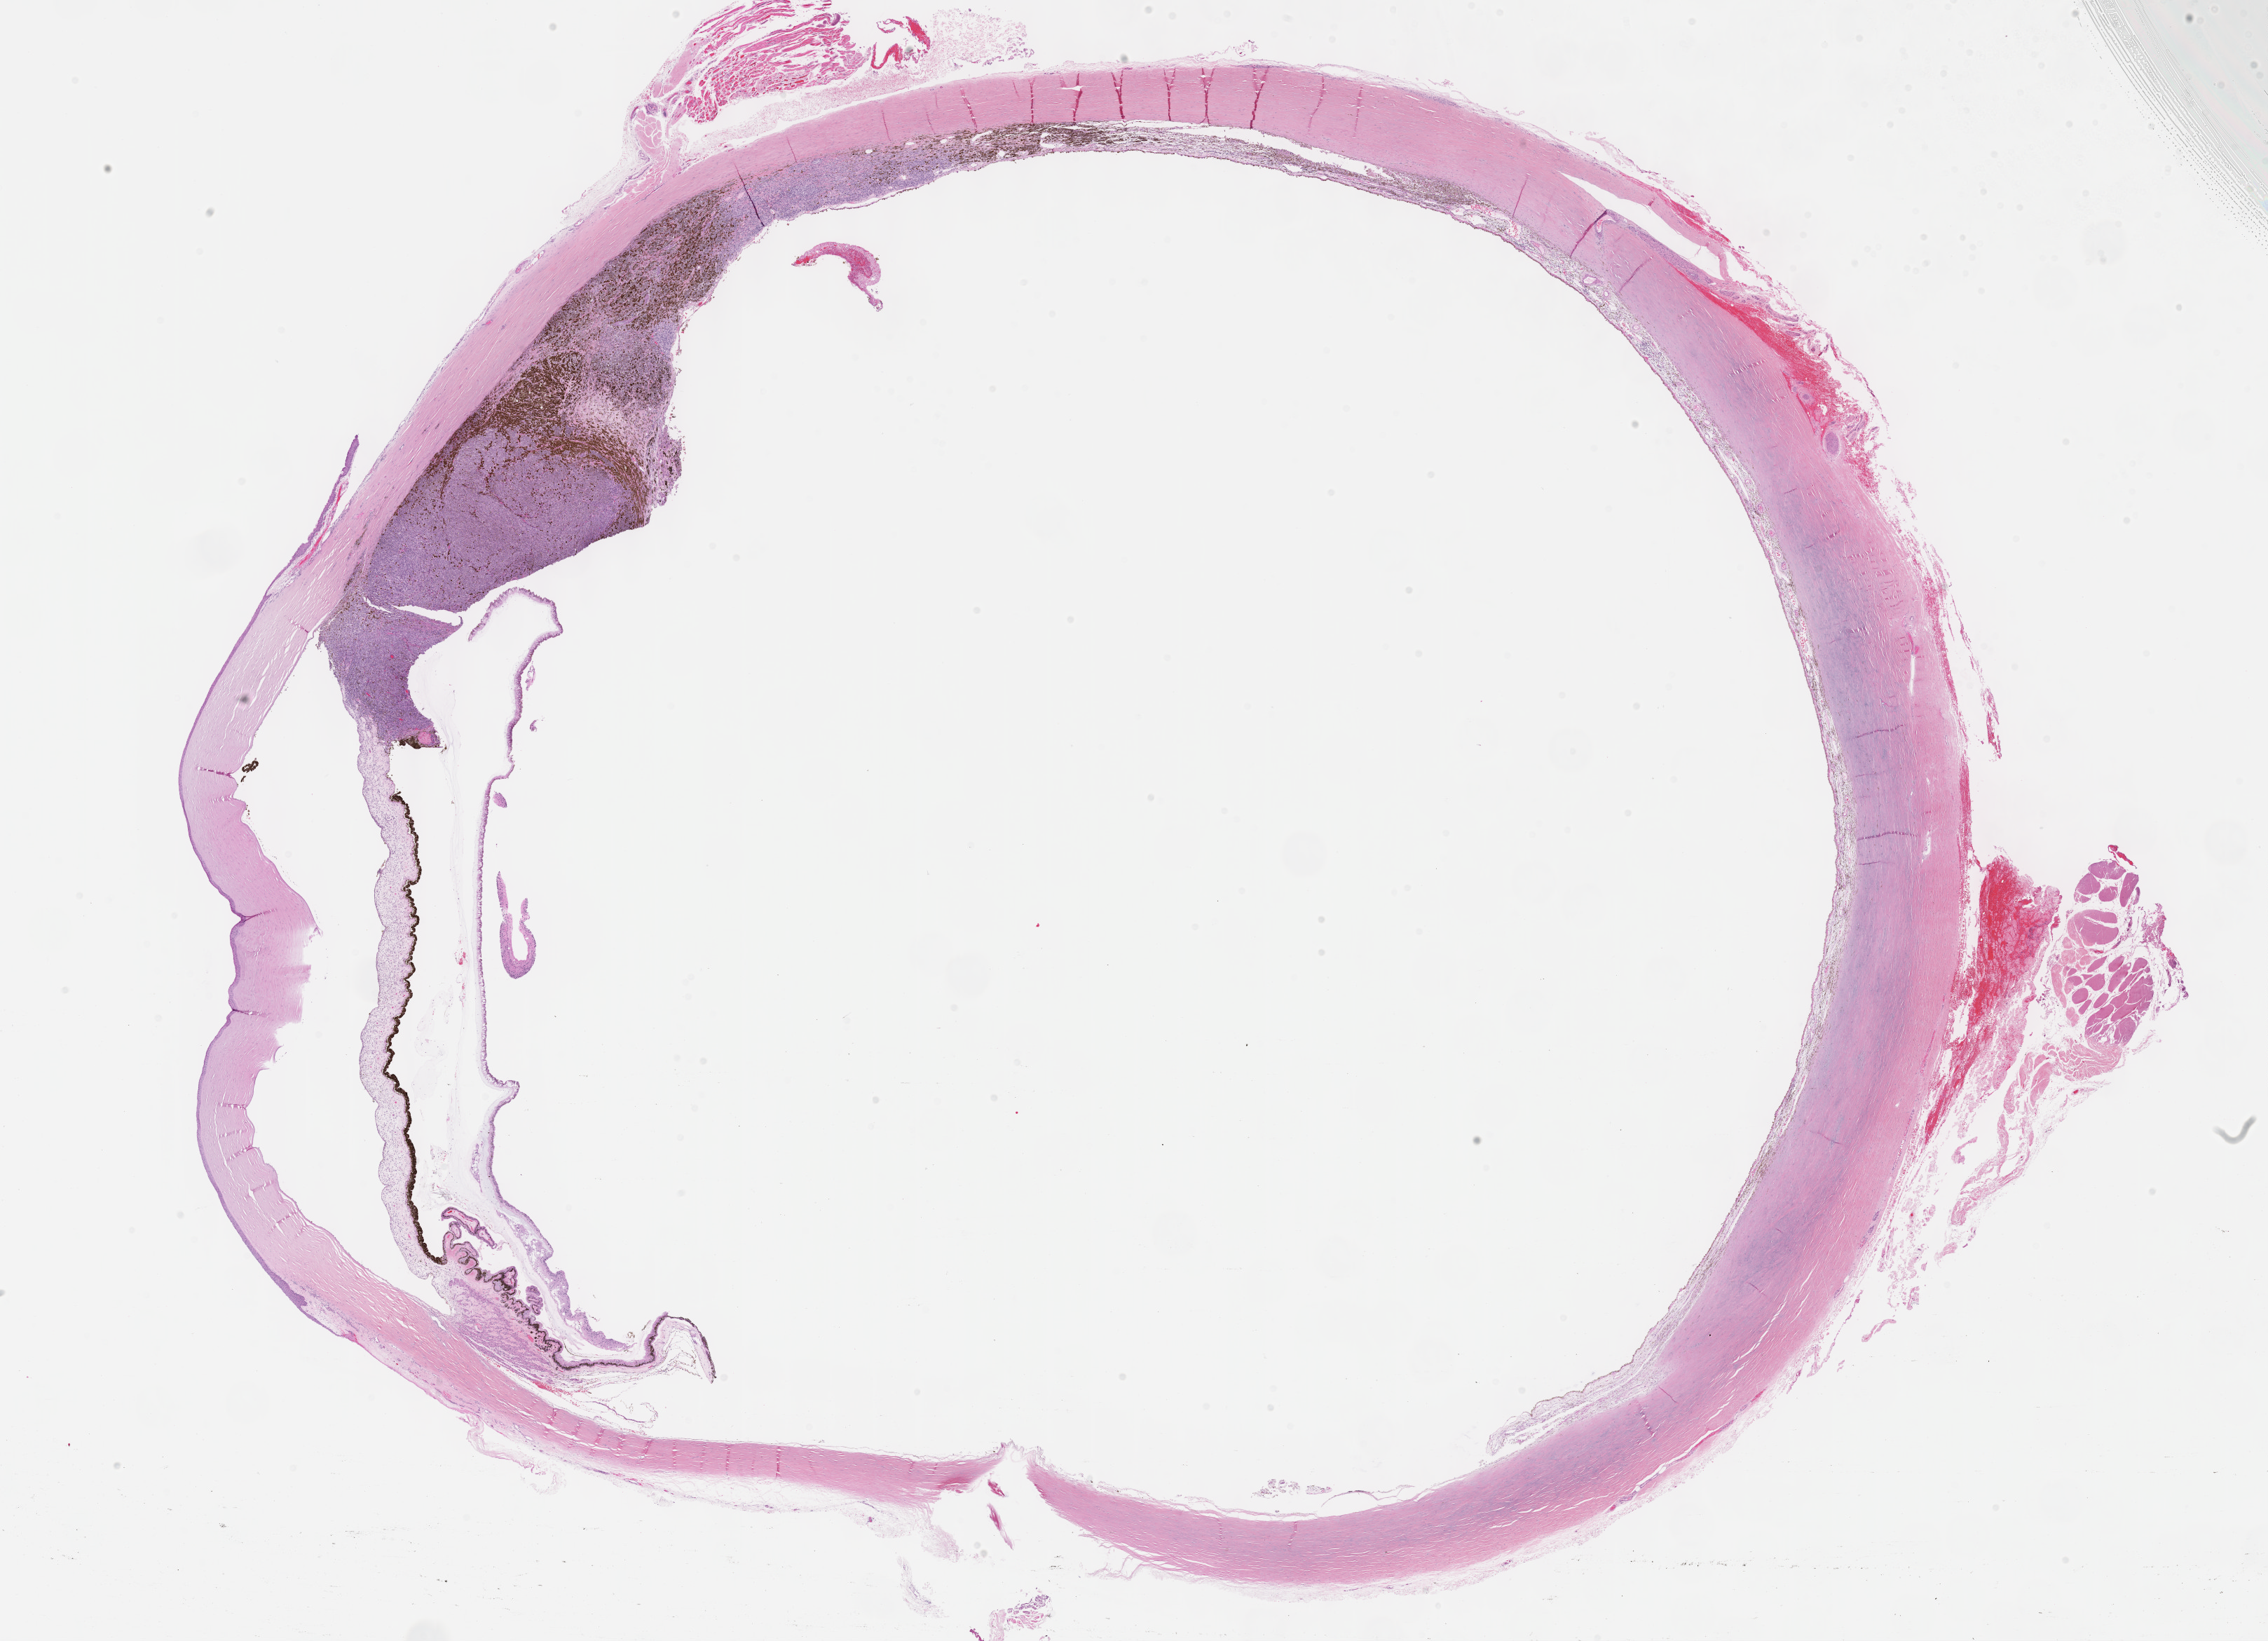
Whole-slide histology image, H&E-stained — shown as a low-resolution overview of the whole scanned area (about 26.2 x 18.9 mm, slide scanned at 40x), formalin-fixed paraffin-embedded (FFPE) diagnostic section, sample: primary tumour, uvea. Patient: female, age at initial diagnosis 76 years.
AJCC pathologic stage: IIIA. Diagnosis: Mixed epithelioid and spindle cell melanoma.